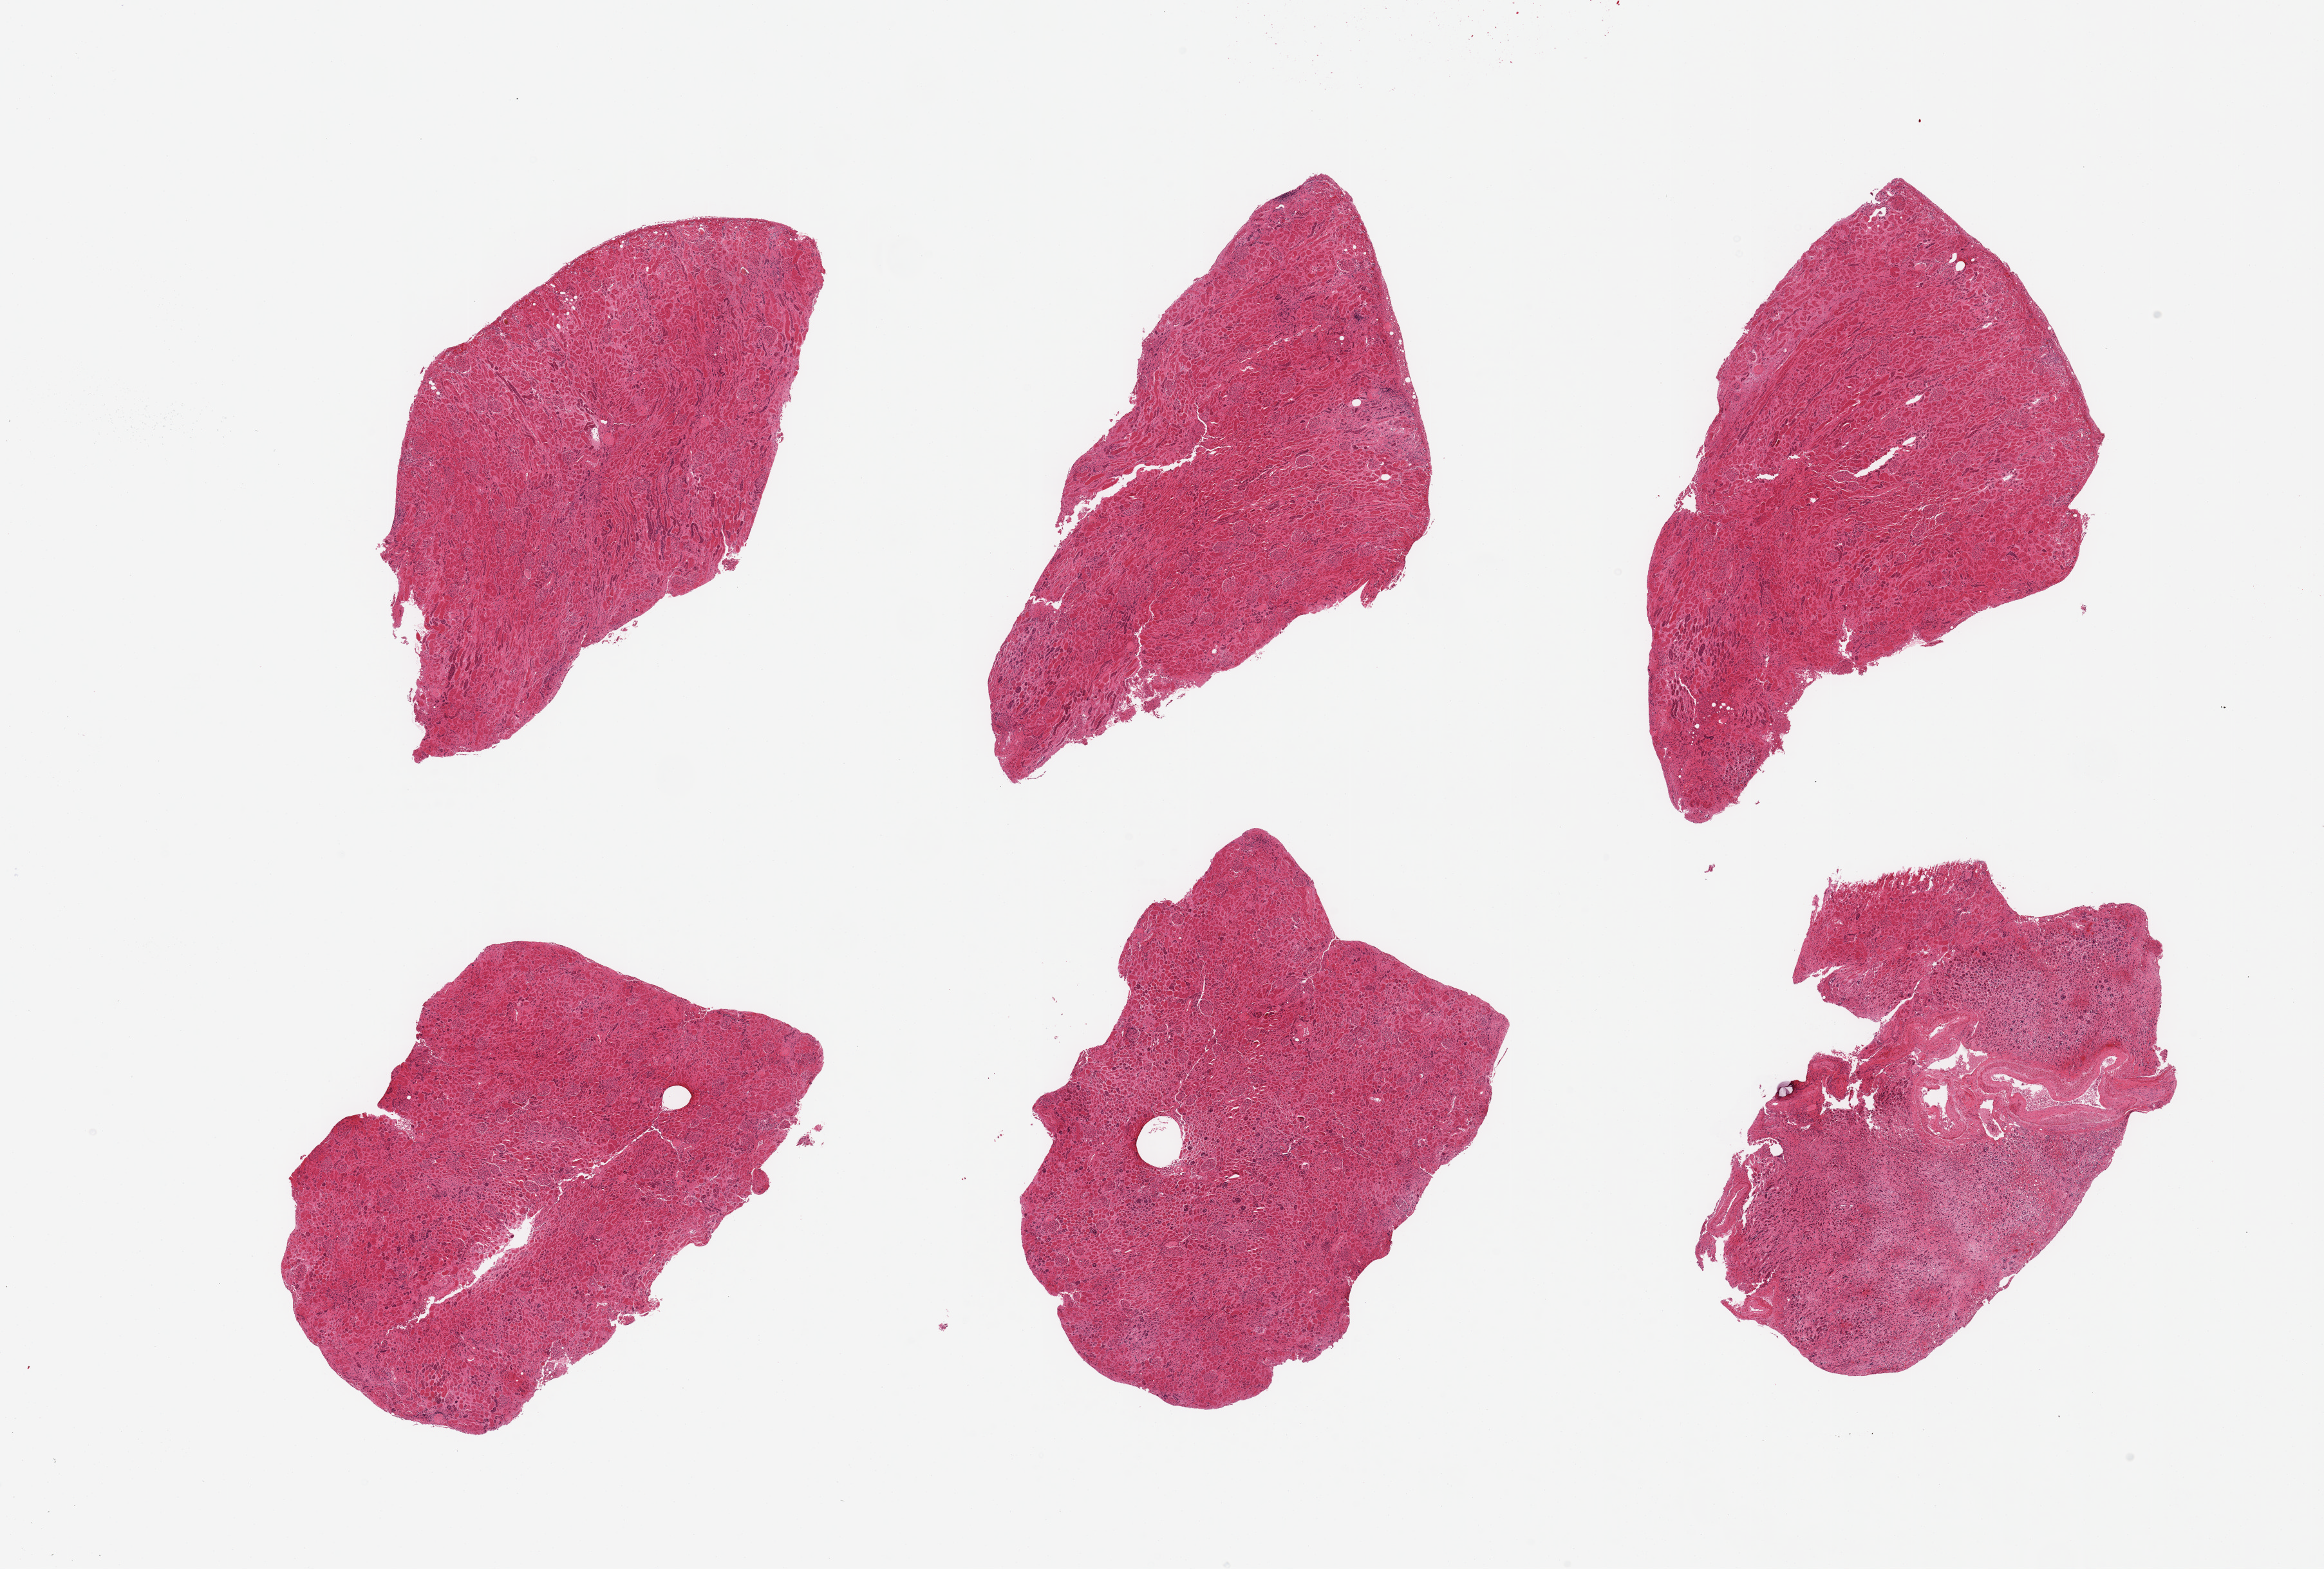
Whole-slide image, H&E stain, shown as a low-resolution overview of the whole scanned area (about 28.5 x 19.3 mm), PAXgene-fixed, paraffin-embedded tissue, section of renal cortex (target tissue), tissue donor sample. Male donor.
- pathologist's review note for this sample: 6 pieces; tubules are very autolyzed, glomeruli (some sclerotic) in all sections, however, 1 of 6 is predominantly medulla